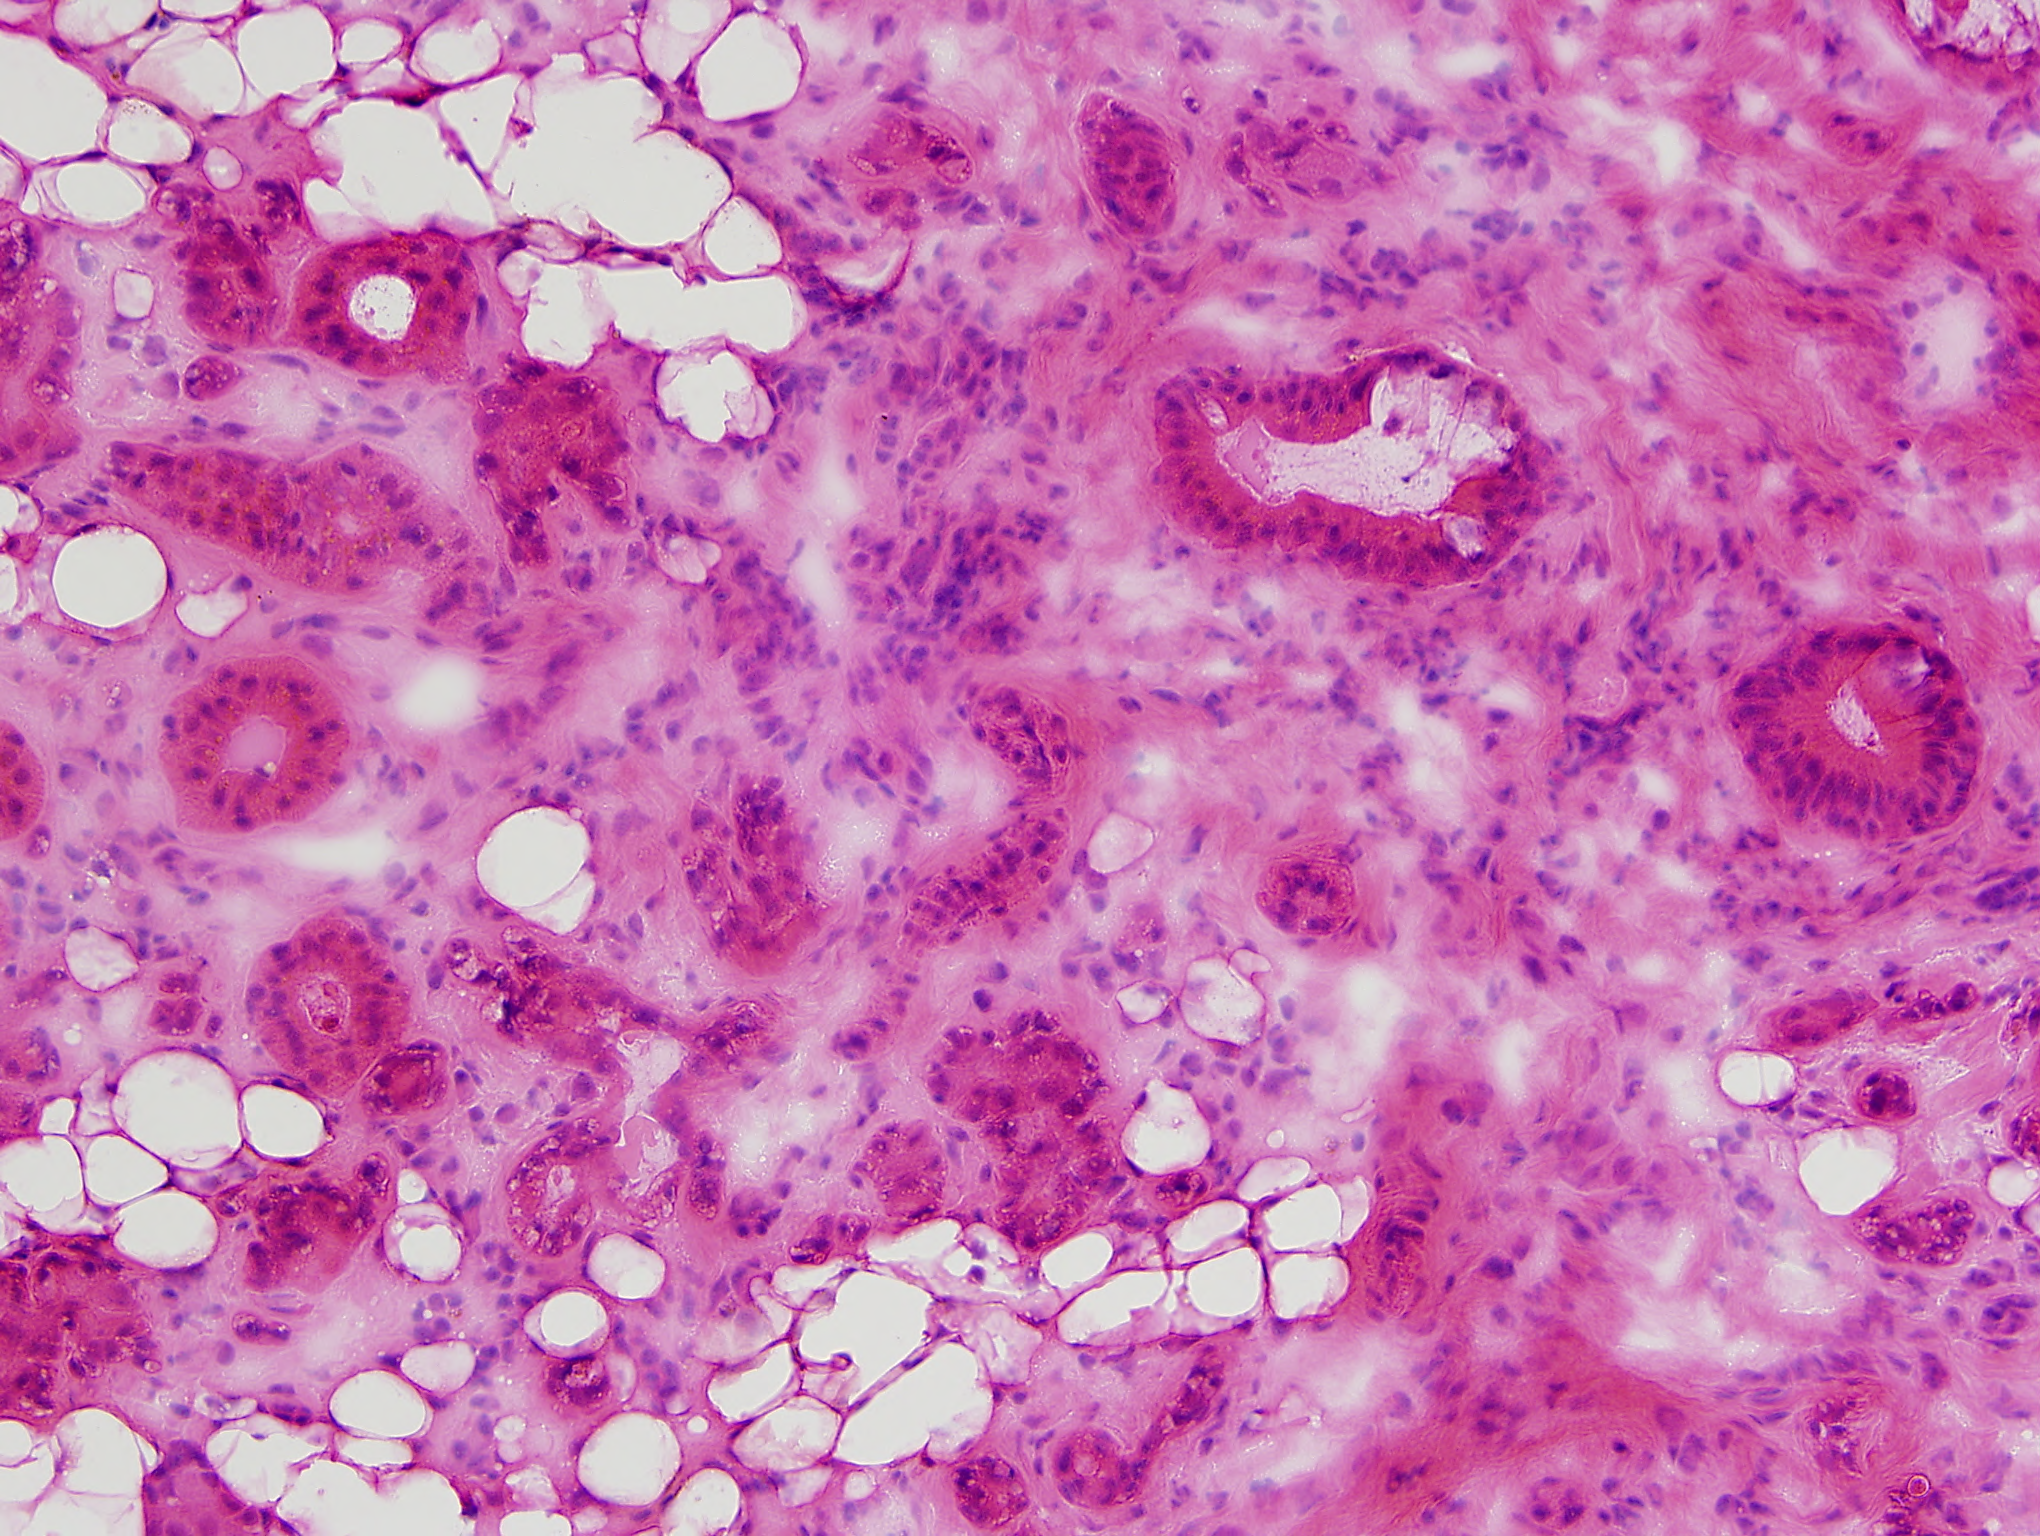
Single-field H&E-stained photomicrograph — about 1.0 x 0.8 mm across, frozen section from the top of the tissue portion, head and neck, solid tissue normal (non-tumour tissue) sample. Male patient; age at initial diagnosis 64 years. Infiltration values recorded for this section: lymphocyte infiltration 5%, monocyte infiltration 1%, neutrophil infiltration 1%.
* this section: solid tissue normal (non-tumour) sample from the same patient
* patient diagnosis: Squamous cell carcinoma, NOS (overlapping lesion of lip, oral cavity and pharynx)